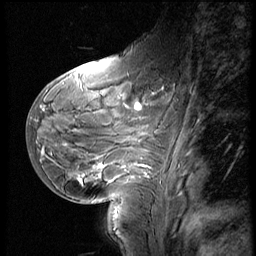
Breast MRI (dynamic contrast-enhanced), one sagittal slice. Slice 23 of 60 in the series (ordered by position). 3 images stored at this slice position (order not interpretable as contrast timing). 1.5 T. TE 4.2 ms, TR 8.9 ms. 2.5 mm slice thickness. 256 × 256 image matrix, field of view 200 × 200 mm. Female patient, age 29 years. Case-level facts recorded for this patient, not image findings: setting: breast cancer imaged before/during neoadjuvant chemotherapy.
Structures marked on this image (semi-automatic segmentation, software-assisted and operator-edited):
- analysis volume of interest (the breast-tissue region the enhancement analysis was run in; not a lesion): box from (x=29, y=57) to (x=182, y=200) px
- tumour enhancement mask (voxels above the 140 % enhancement threshold inside the analysis volume of interest): (x=80, y=105)–(x=141, y=181)